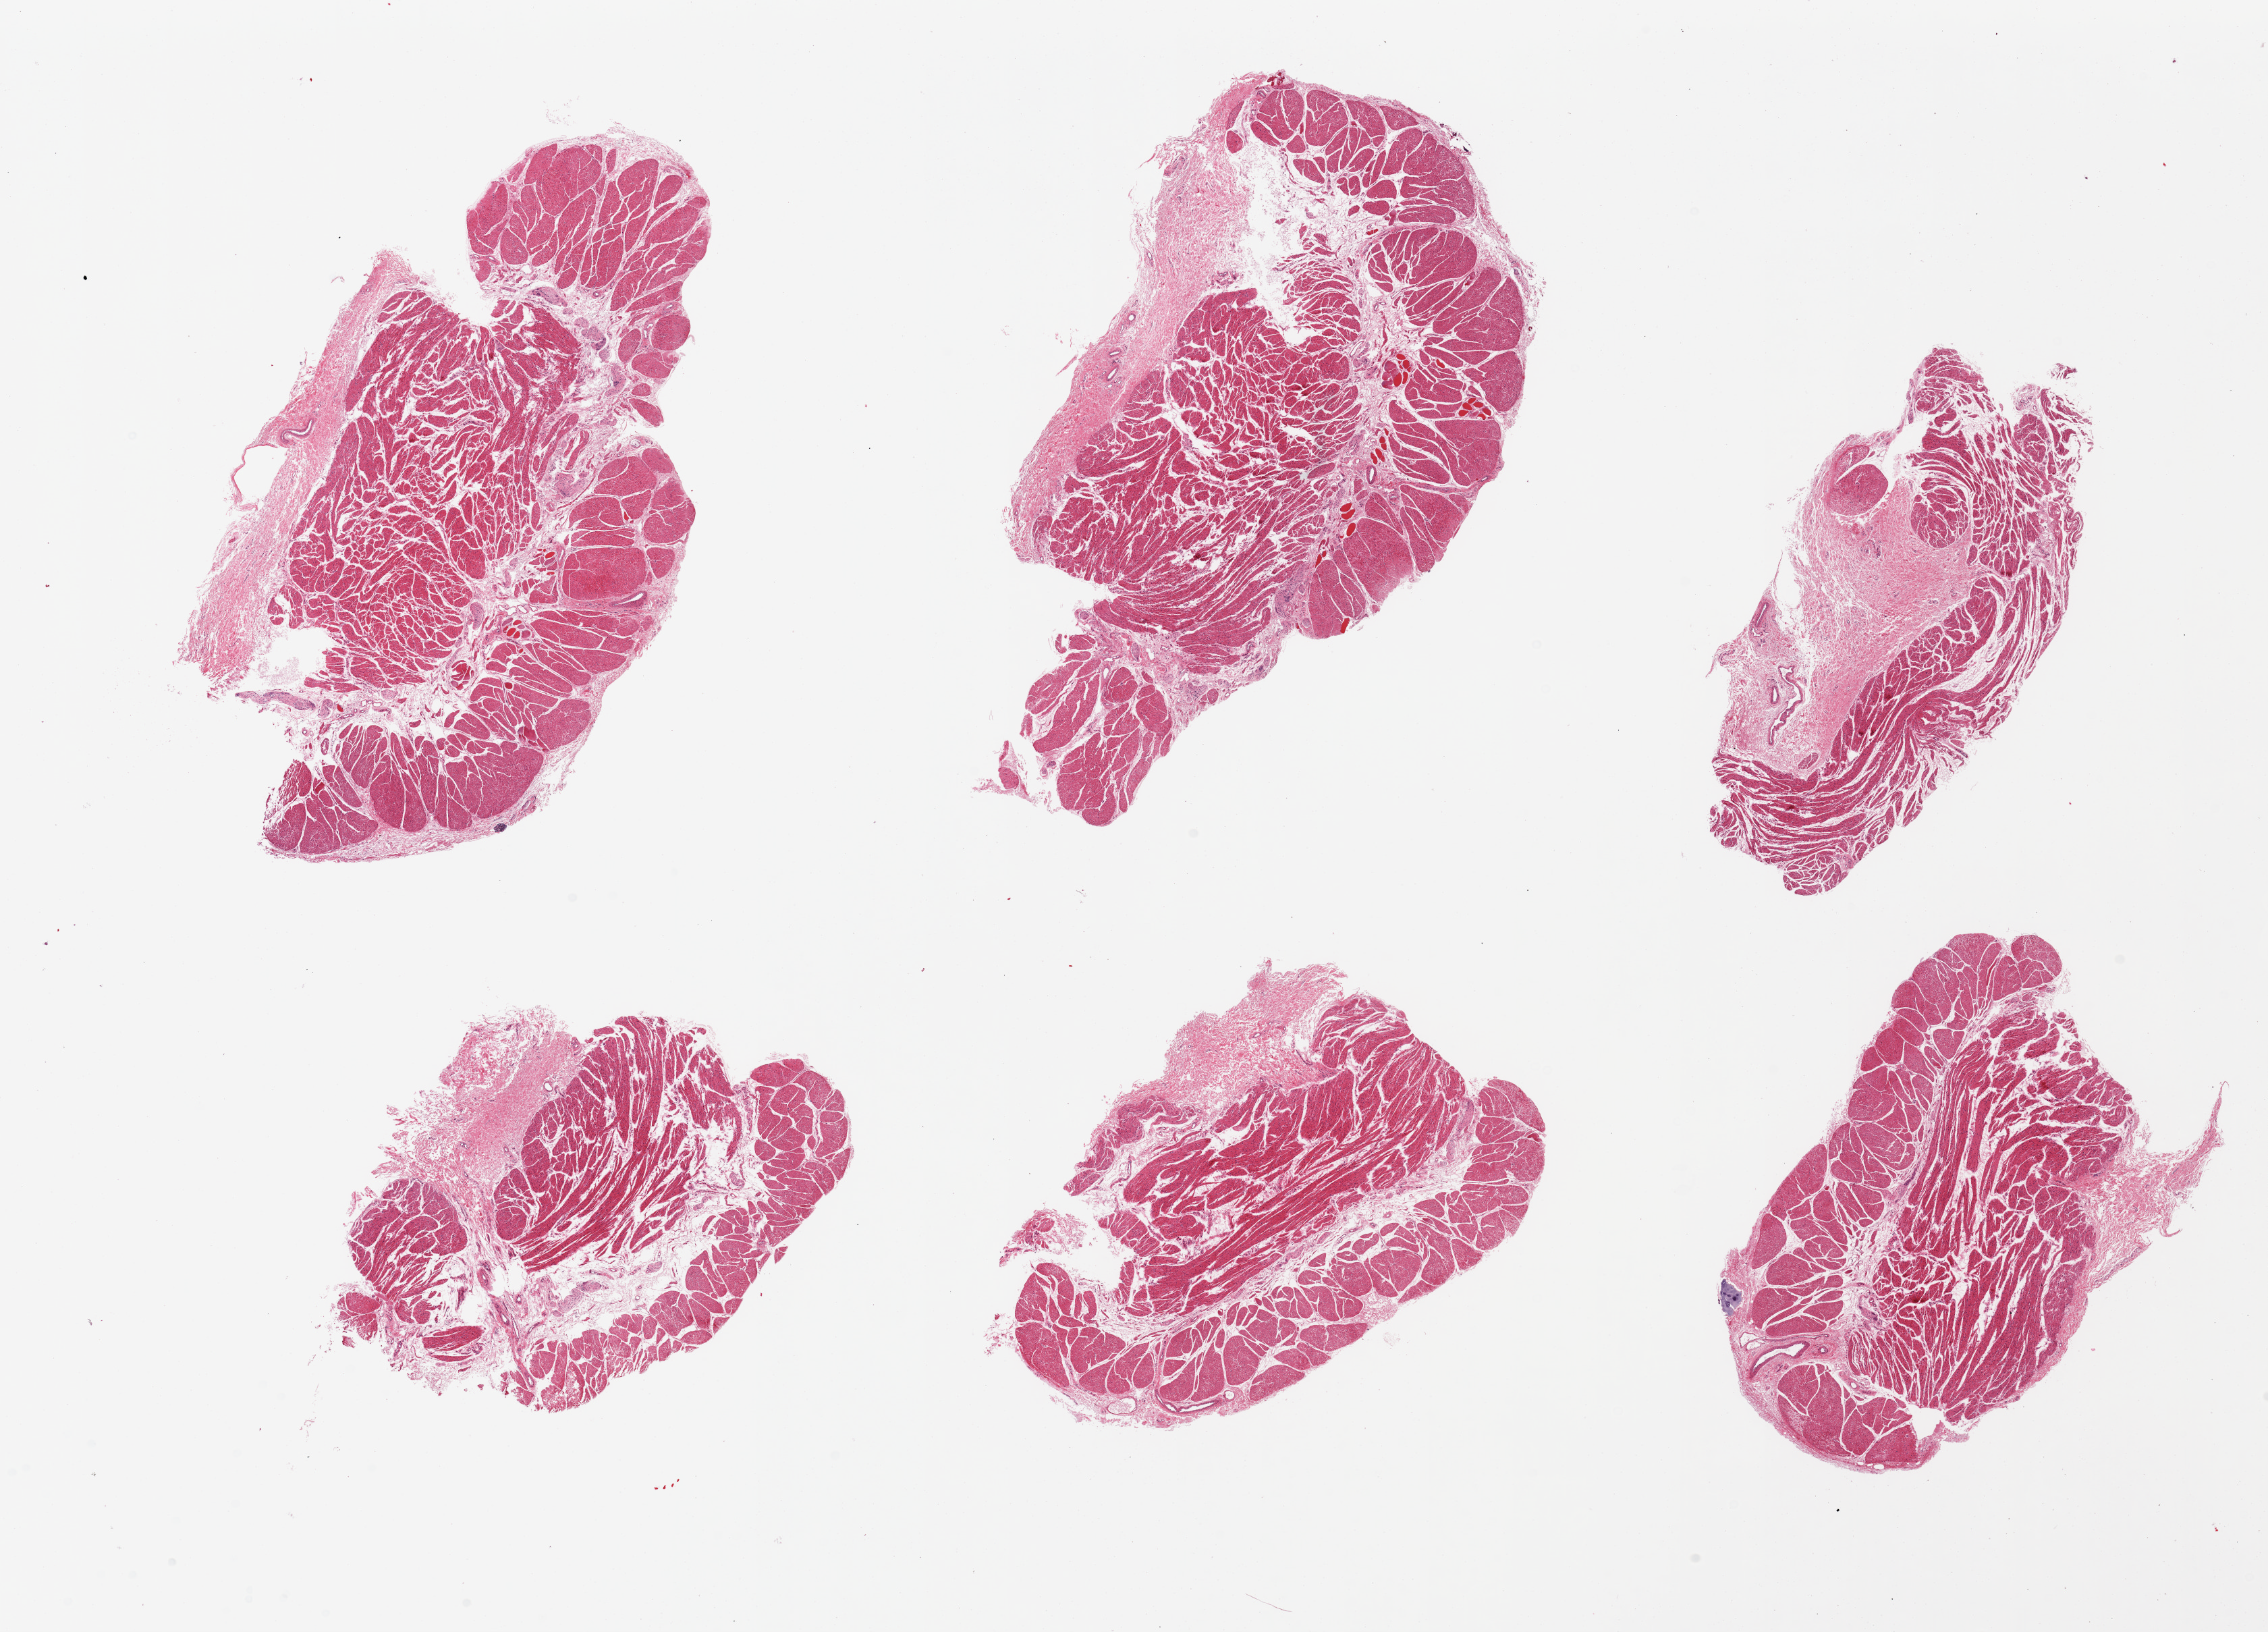
Hematoxylin and eosin (H&E) whole-slide image — a low-resolution overview of the entire scanned area, about 26.6 x 19.1 mm (slide scanned at 20x), PAXgene-fixed paraffin-embedded (PFPE) section, sampled site (target tissue): esophageal muscle, donor tissue sample. Donor: male.
Reviewer comment on this tissue sample: 6 pieces. Up to 30% fibrous stroma.